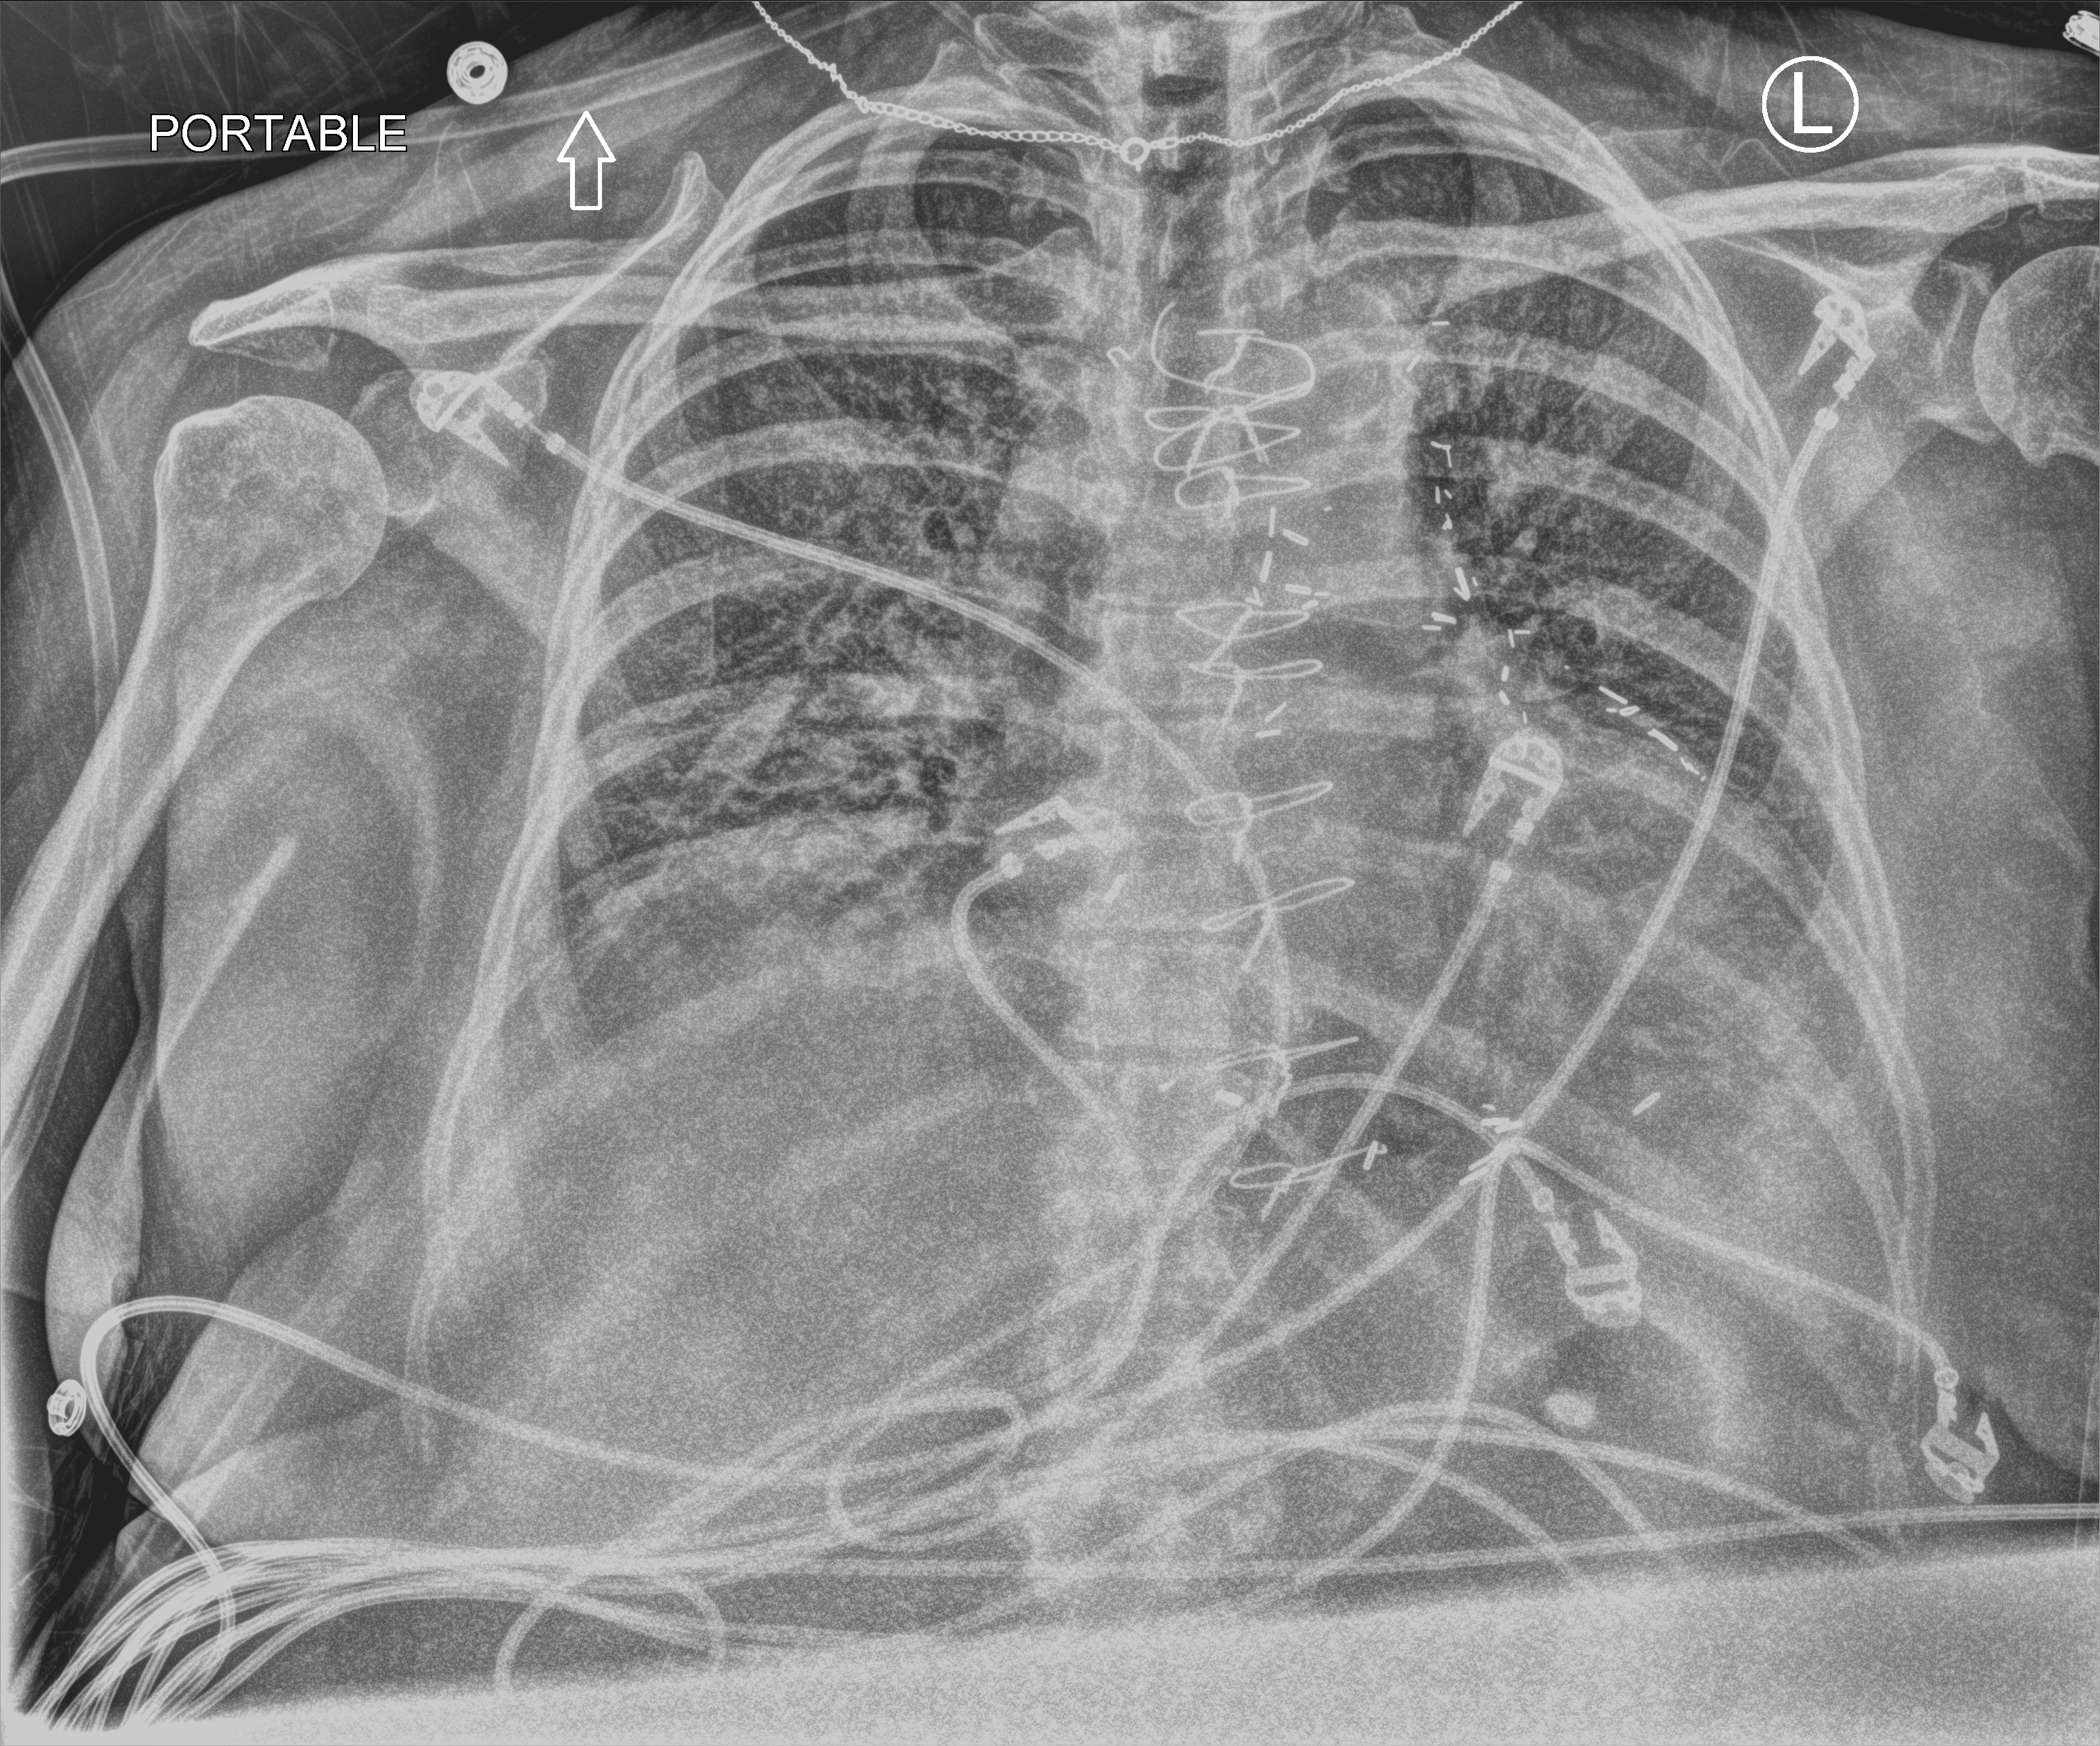
Chest X-ray (portable), anteroposterior (AP) projection. Patient hospitalised with COVID-19; female, aged 60–74 years.
Admission-level facts for this patient (not findings on this image; timing relative to this image not recorded):
- chronic kidney disease (admission record): no
- mechanically ventilated during this hospital stay: yes
- diabetes (admission record): no